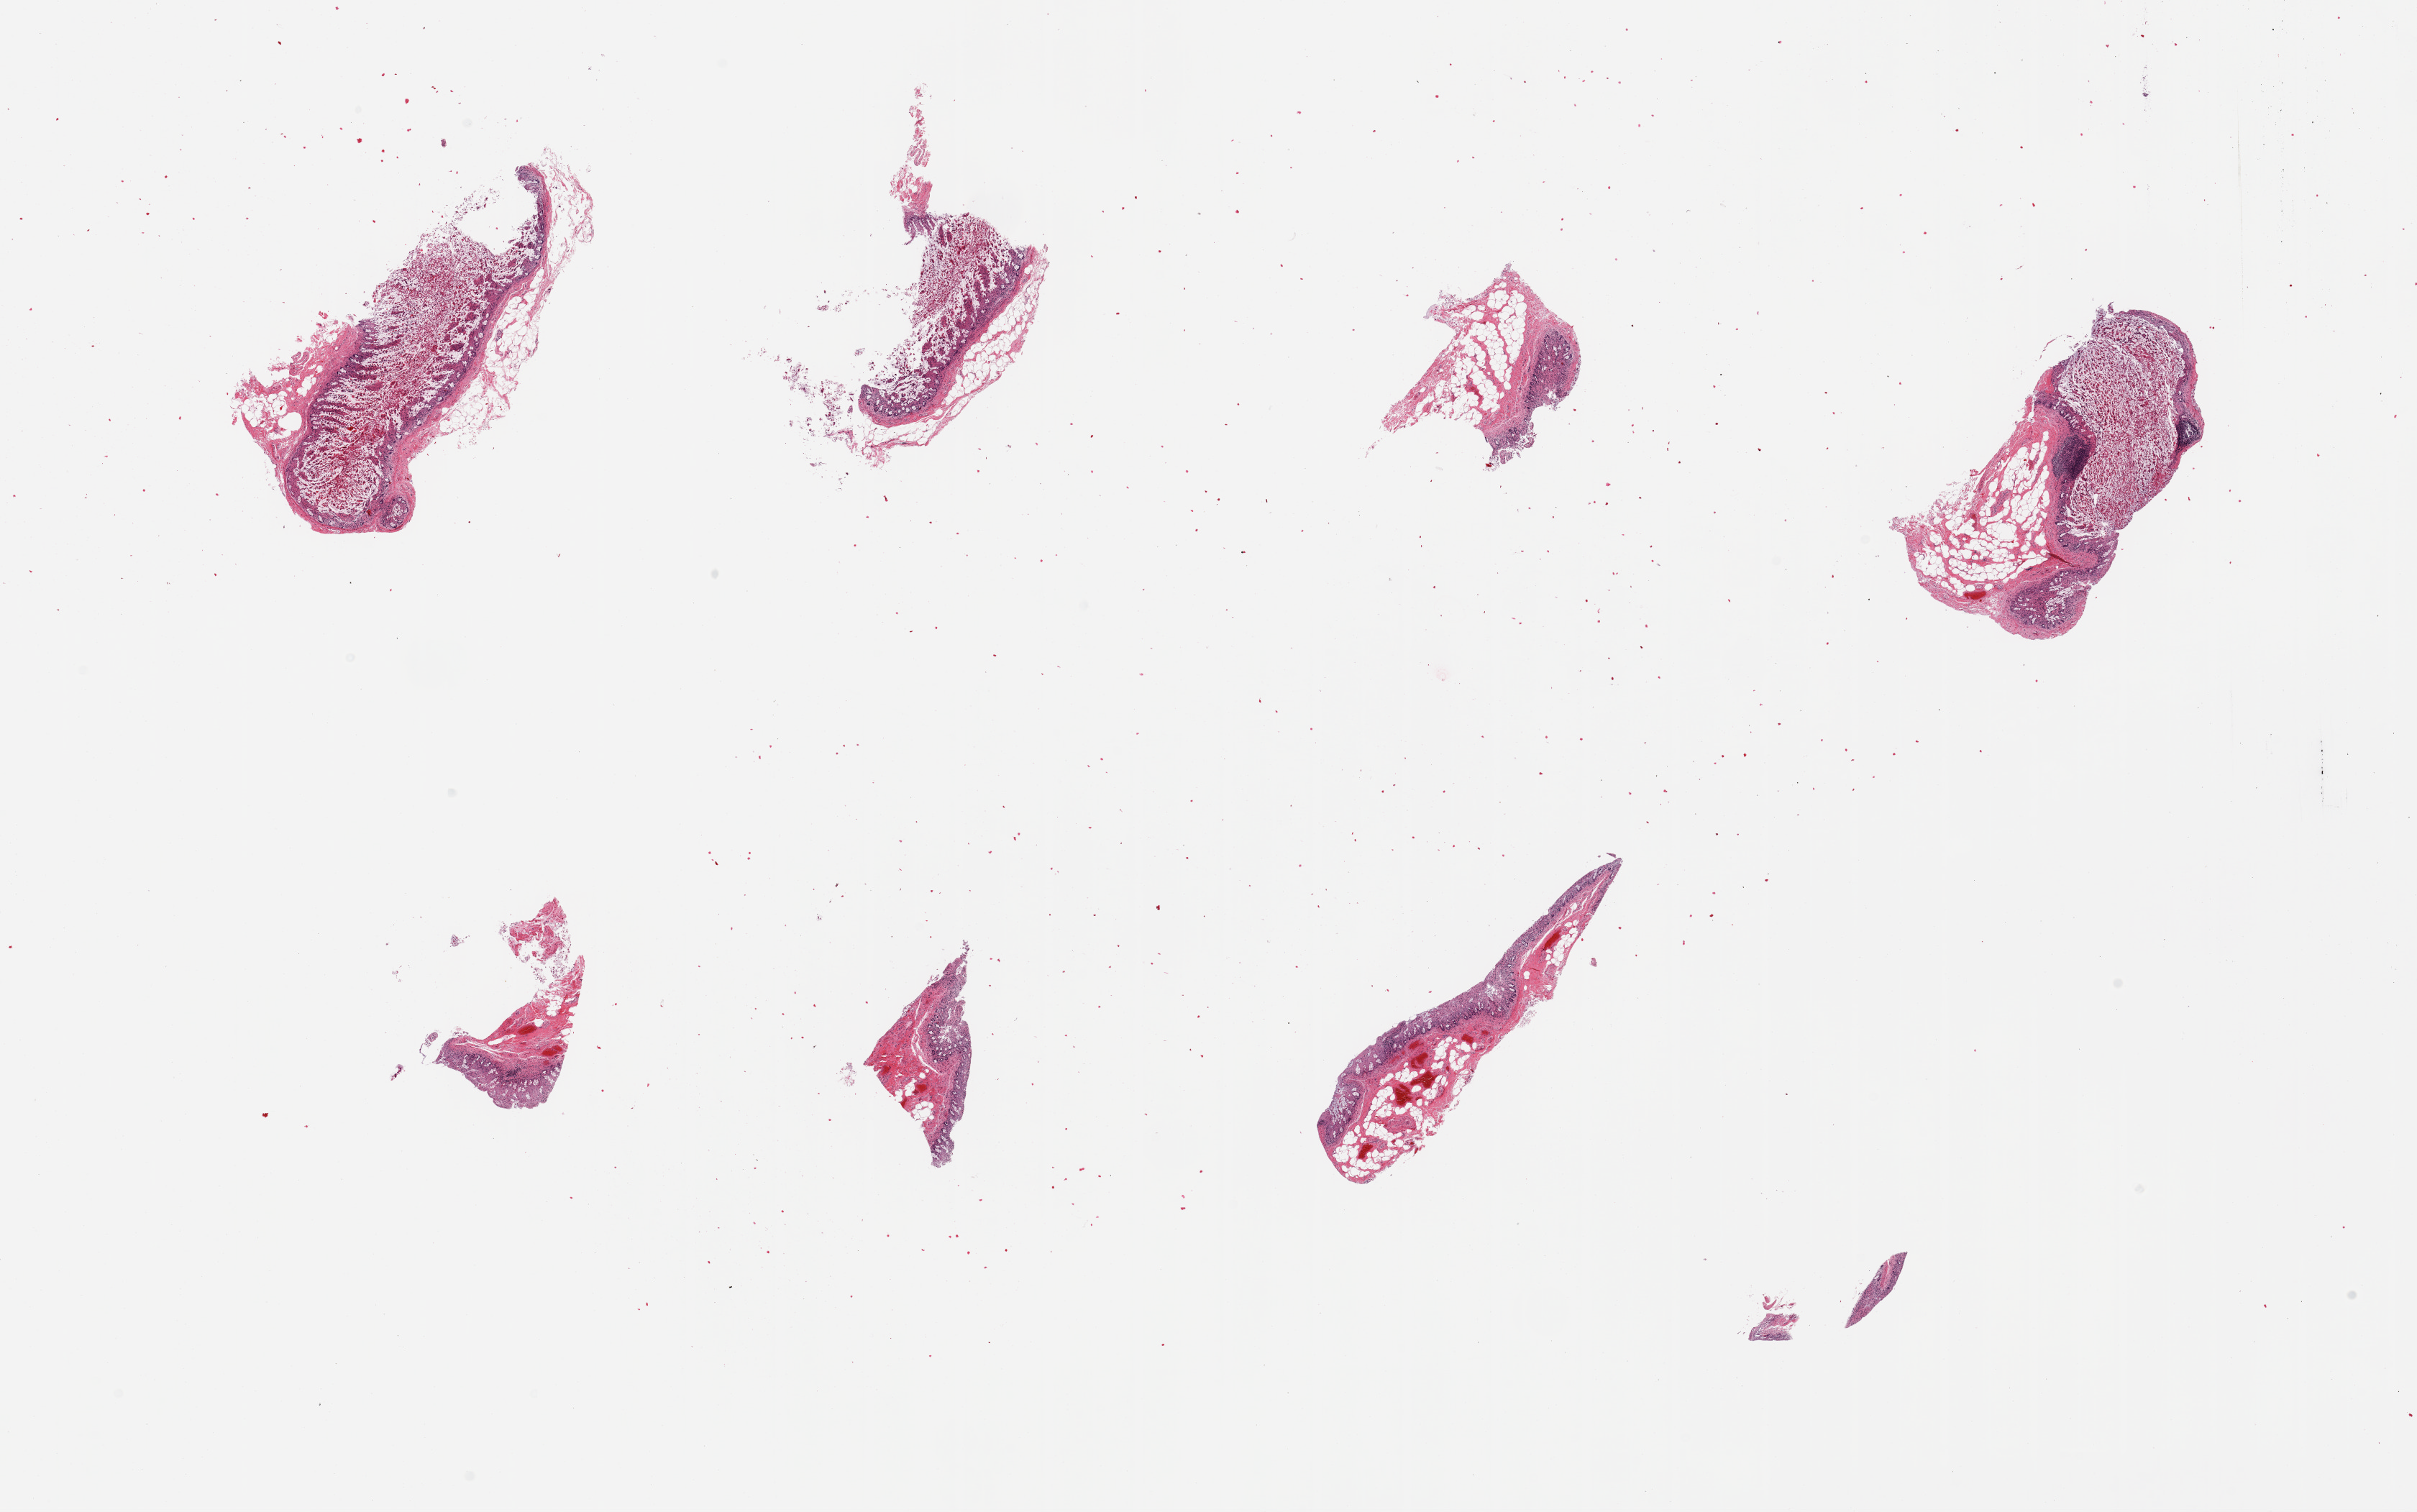
Digitized haematoxylin and eosin-stained section — a low-resolution overview of the entire scanned area, about 26.6 x 16.6 mm (acquisition: 20x scan).
Specimen: PAXgene-fixed paraffin-embedded (PFPE) section; sampled site (target tissue): ileum; donor tissue sample.